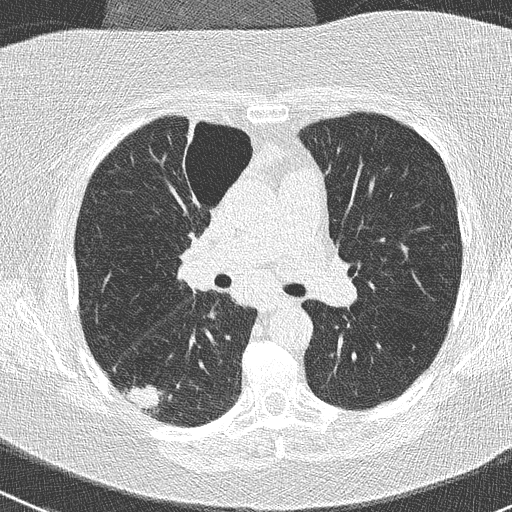
Low-dose screening chest CT, axial slice. Baseline annual screen. Lung window (W 1500 / L -600 HU). 2 mm slice thickness. Slice 105 of 261 in the series. 512 × 512 image matrix, field of view 310 × 310 mm. Female, age 74 years at enrolment.
Expert reader's lesion annotation, bounding box [x1, y1, x2, y2] px = [115, 378, 173, 424]. The screening reader recorded 3 non-calcified nodules or masses ≥4 mm on this exam (right lower lobe, right upper lobe, left lower lobe); which of them this box marks is not recorded. Official screen result: positive, change unspecified: nodule(s) >= 4 mm or enlarging nodule(s), mass(es), or other non-specific abnormalities suspicious for lung cancer. Lung cancer was diagnosed 16 days after this screen: non-small cell carcinoma, right lower lobe, poorly differentiated (G3), stage IIIA (AJCC 6th edition), 28 mm at pathology.